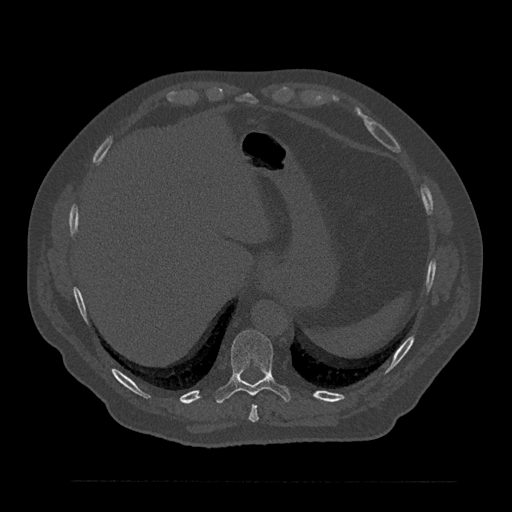
CT including the spine, one axial slice. Position 355 of 797 along the scan axis. 120 kVp. Bone window (W 1800 / L 400 HU). 0.5 mm slice thickness. 512 × 512 image matrix, field of view 430 × 430 mm. Patient: male, 61 years. Case-level facts recorded for this patient, not image findings: primary cancer: prostate.
Outlined on this slice (semi-automatically segmented with operator editing):
- T10 vertebra: bounding box (x1, y1, x2, y2) in pixels: (215, 329, 291, 404)
- T9 vertebra: (249, 405, 259, 422)